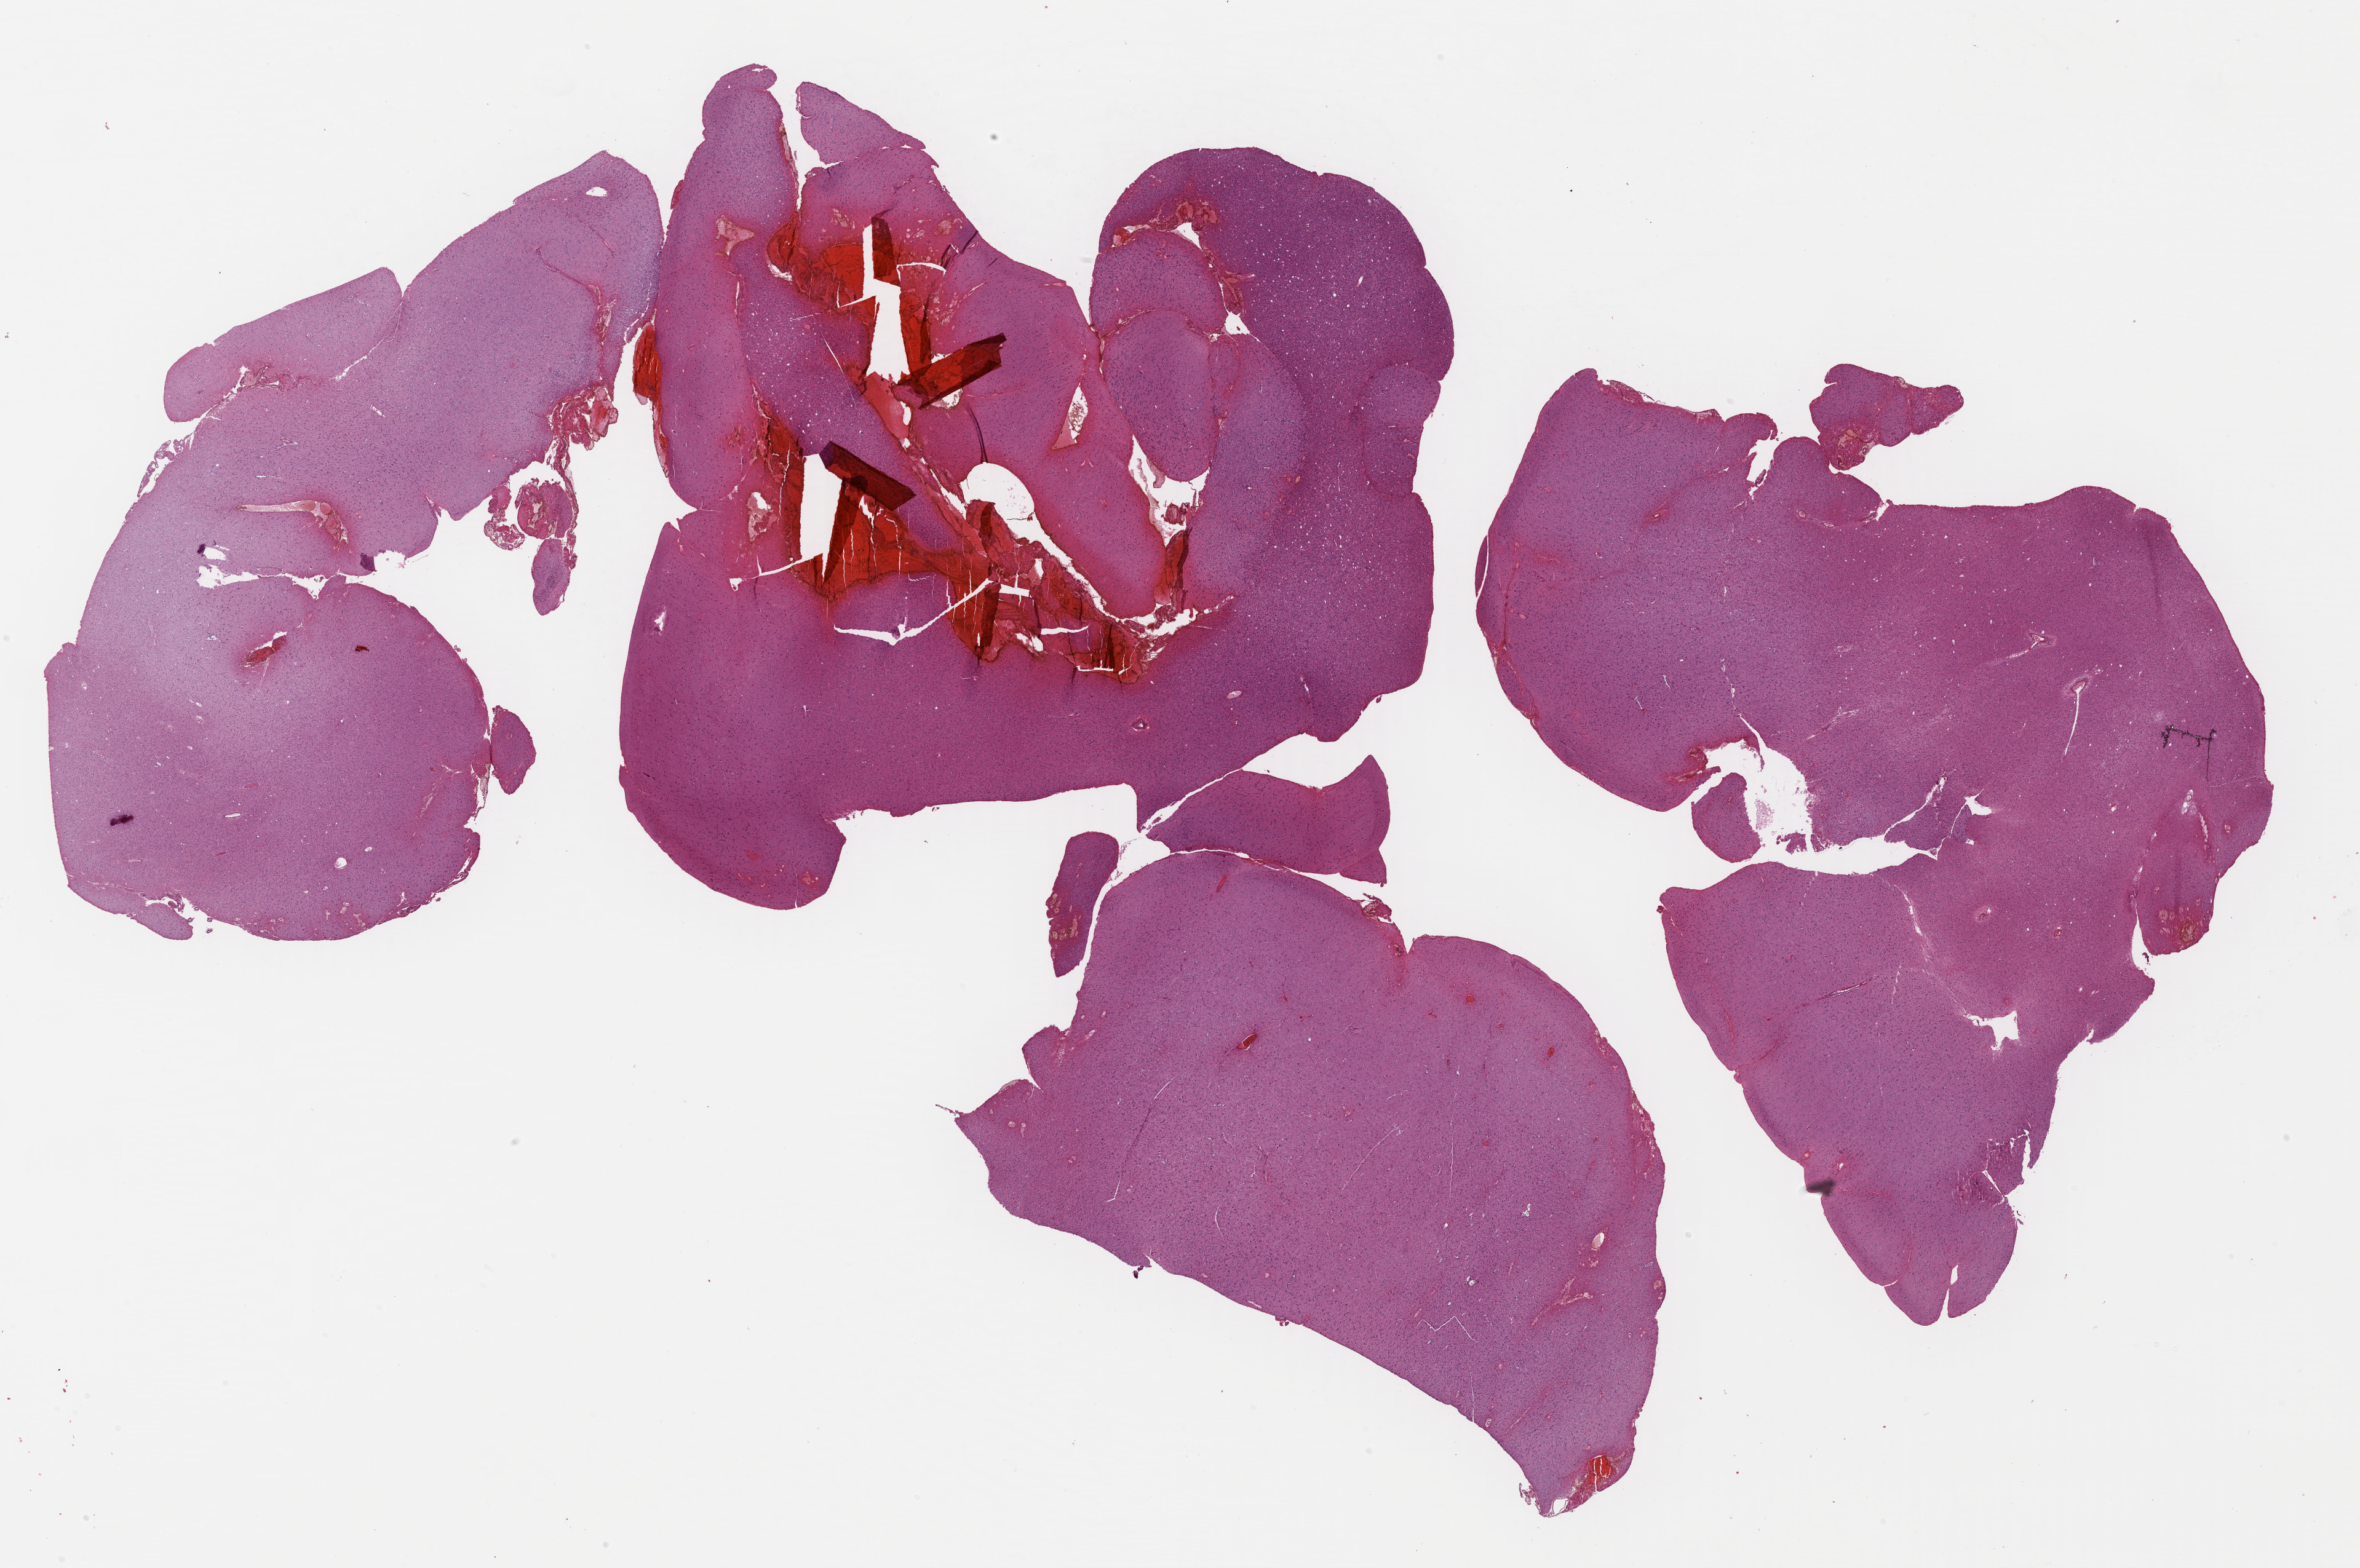
Digitized H&E tissue section (whole slide), low-resolution overview of the scanned area, about 30.2 x 20.0 mm. Formalin-fixed paraffin-embedded (FFPE) diagnostic section. Sample: primary tumour, brain. Female, age 20 years at initial diagnosis. Histologic grade: G2 (moderately differentiated).
Diagnosis: Oligodendroglioma, NOS (cerebrum).